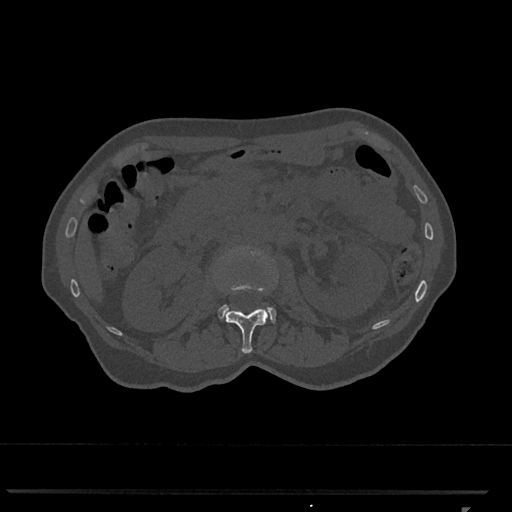
CT including the spine, one axial slice. Position 378 of 793 along the scan axis. Reconstruction kernel Br40s/3. 120 kVp. Bone window (W 1800 / L 400 HU). 0.5 mm slice thickness. 512 × 512 image matrix, field of view 380 × 380 mm. Female patient, age 62 years. From the clinical record (not read from this slice): primary cancer: renal.
Outlined on this slice (semi-automatic segmentation, software-assisted and operator-edited):
- L1 vertebra: bounding box (x1, y1, x2, y2) in pixels: (225, 284, 268, 354)
- L2 vertebra: (218, 247, 276, 323)